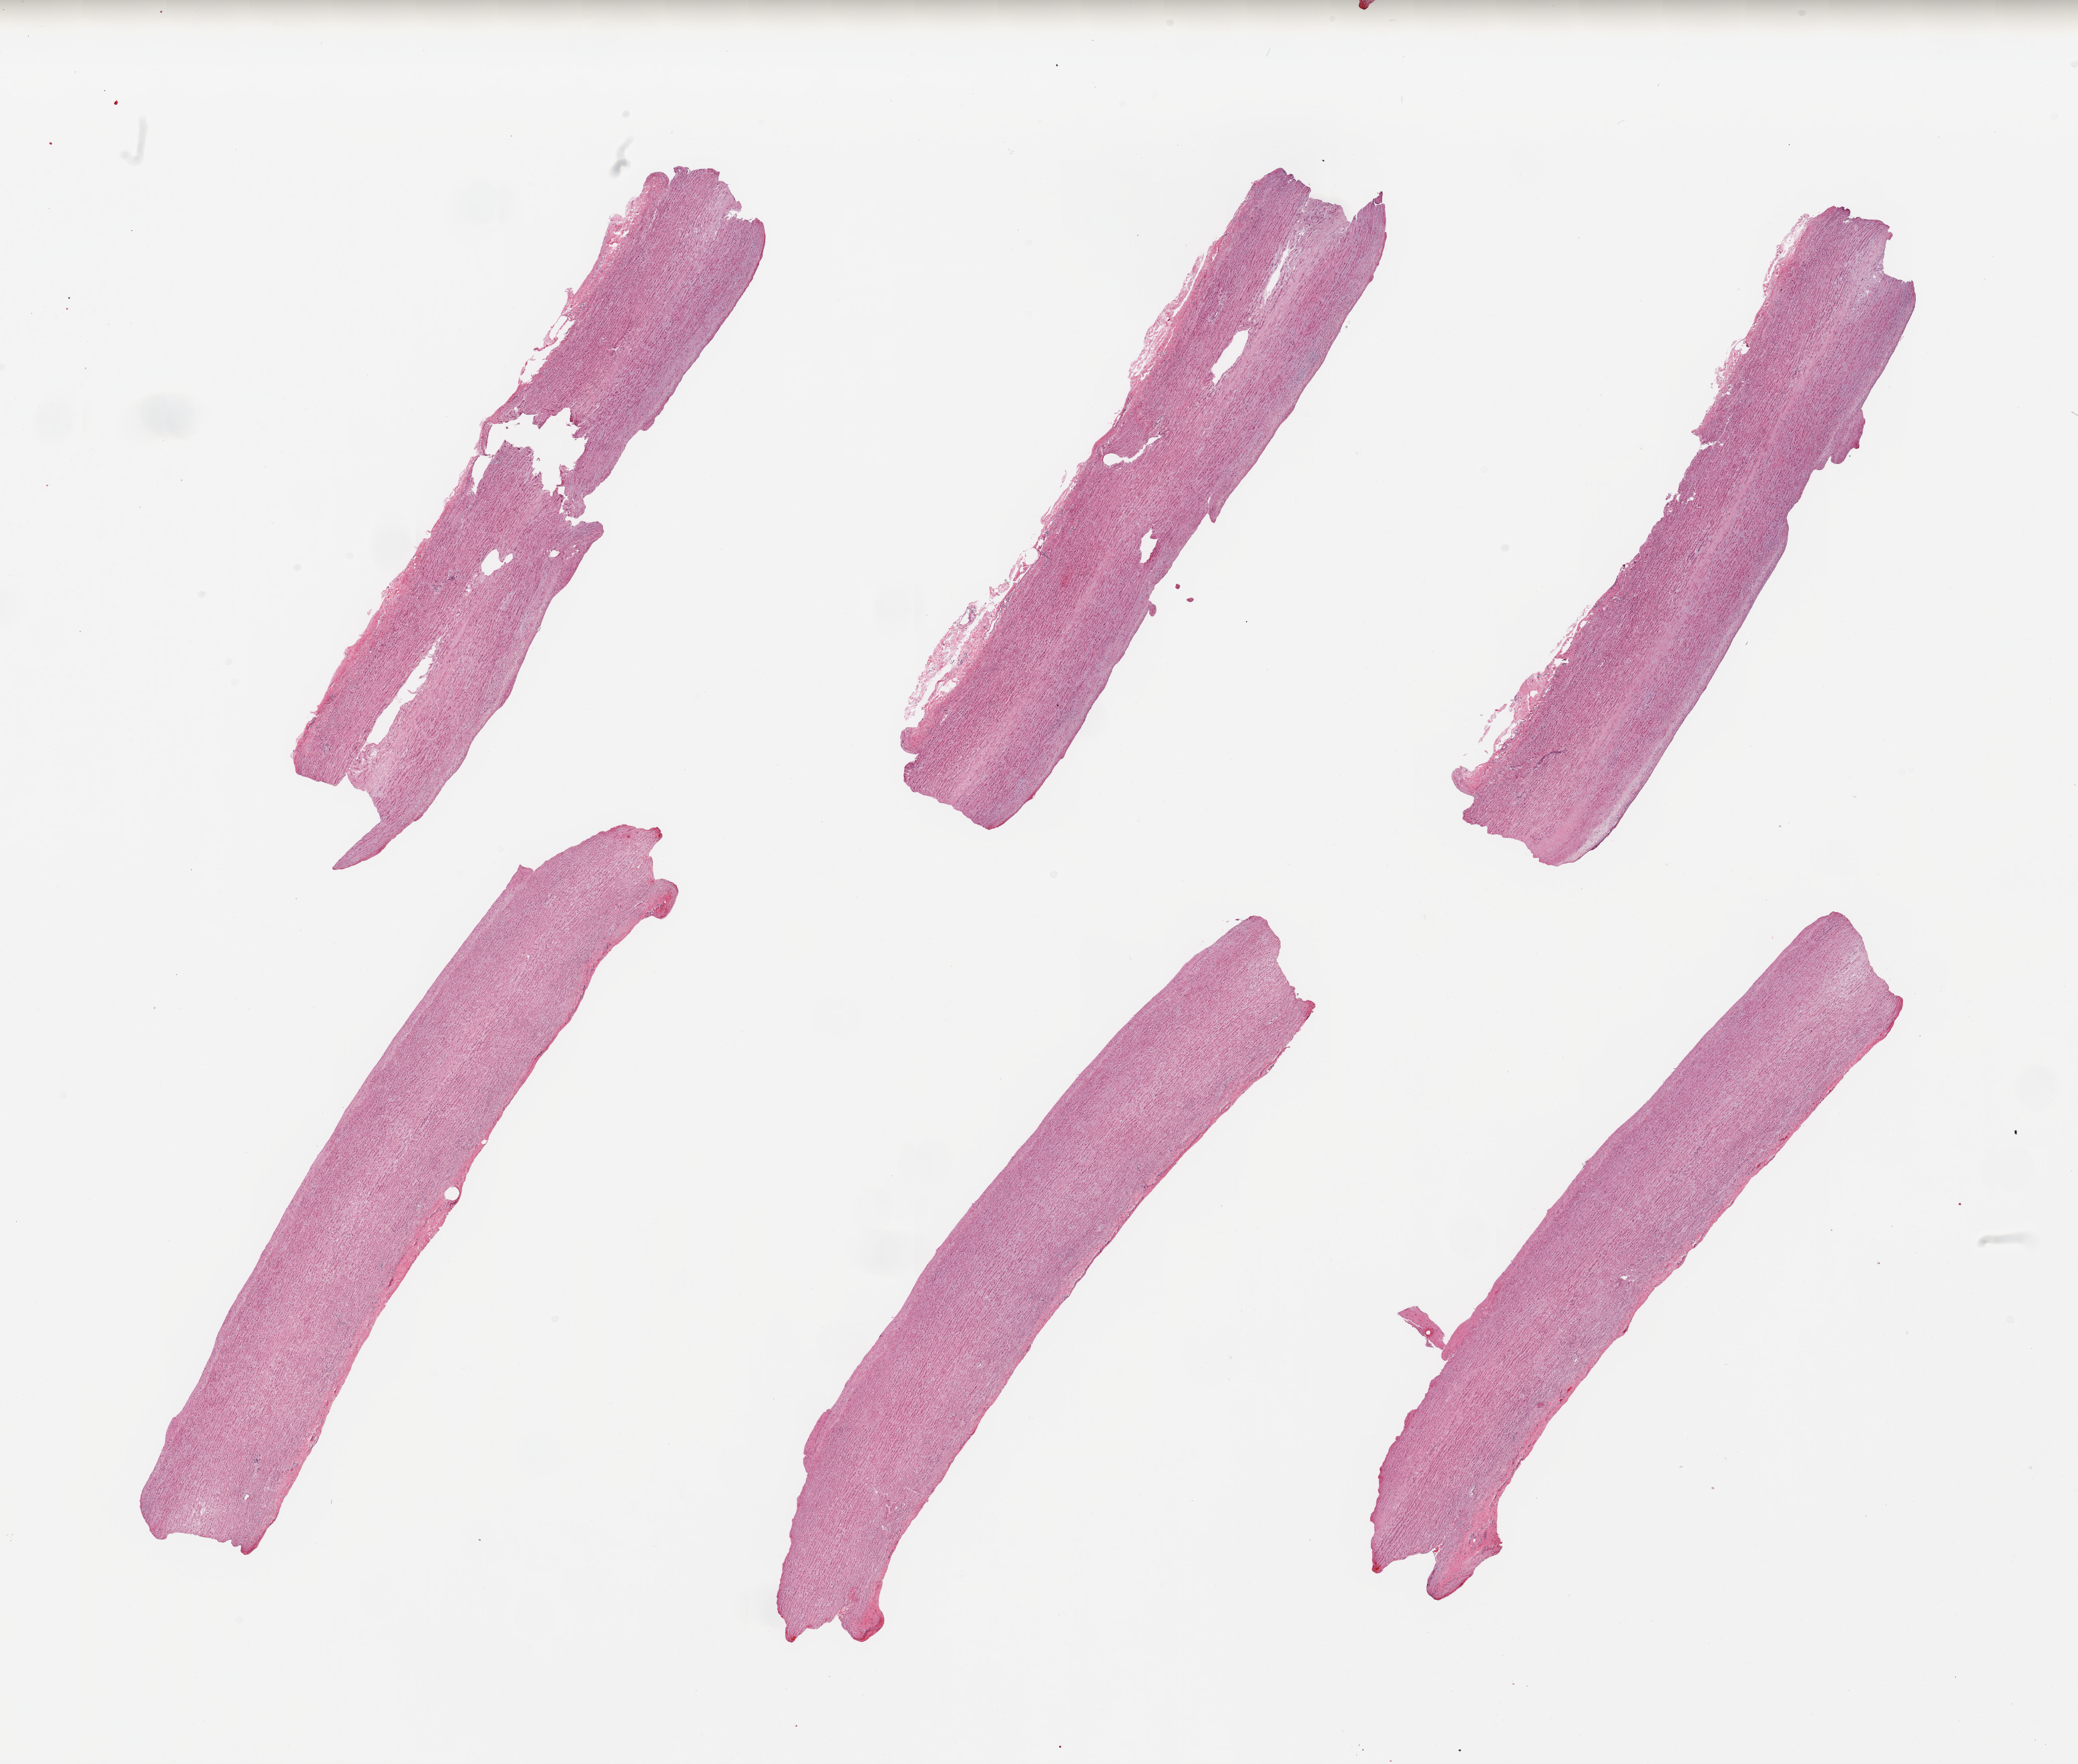
H&E whole-slide image — a low-resolution overview of the entire scanned area, about 24.6 x 20.9 mm, PAXgene-fixed paraffin-embedded (PFPE) section, section of aorta (target tissue), tissue donor sample. Female donor.
Pathologist's review note for this sample: 6 pieces, minimal atherosis.